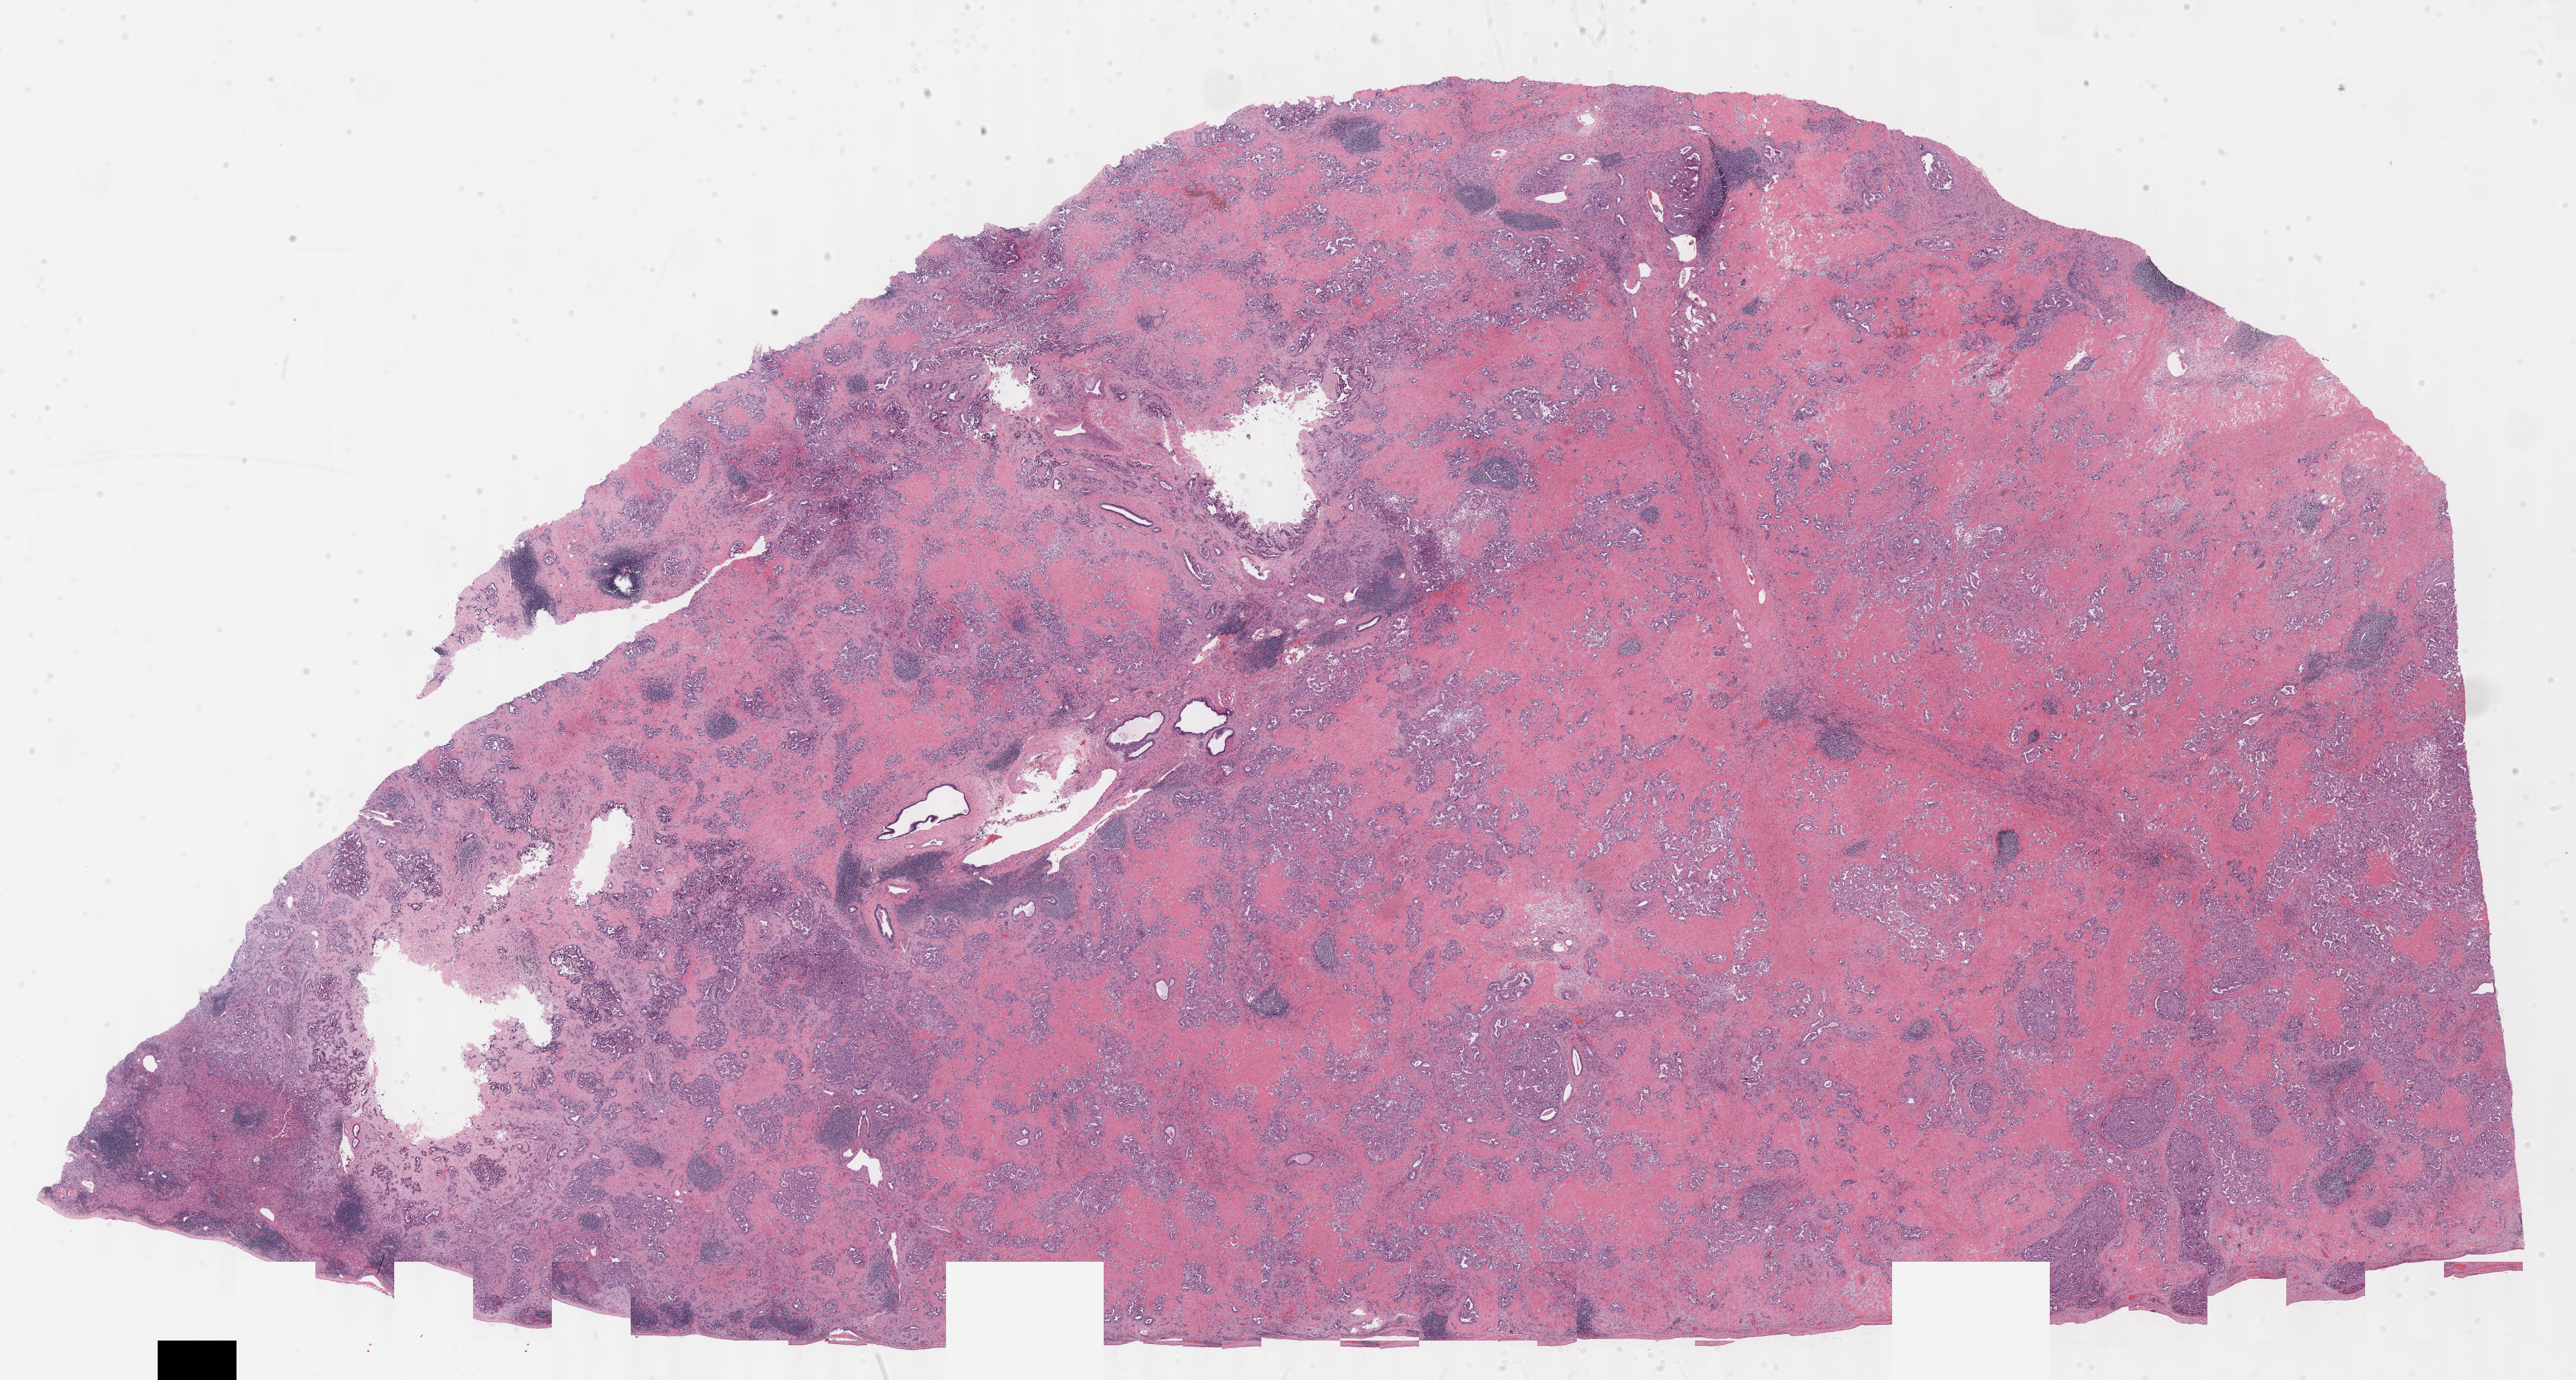
Whole-slide histology image, H&E — shown as a low-resolution overview of the whole scanned area (about 31.7 x 17.0 mm); formalin-fixed paraffin-embedded (FFPE) diagnostic section; sample: primary tumour, bile duct. Patient: female, age at initial diagnosis 50 years. Histologic grade: G2 (moderately differentiated).
Histologic diagnosis: Cholangiocarcinoma. TNM: T2b NX M0. AJCC pathologic stage: II.